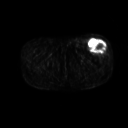
FDG PET of an extremity soft-tissue mass (from a PET/CT study), one axial slice; position 232 of 267 along the scan axis; 3.27 mm slice thickness; 128 × 128 image matrix, field of view 500 × 500 mm. Patient: male, 64 years. Case-level facts recorded for this patient, not image findings: histological type: extraskeletal osteosarcoma; grade: high; site of the primary tumour: thigh.
Annotated regions visible in this slice (expert contour drawn on MRI and transferred to this co-registered scan by the dataset authors):
- gross tumour volume (mass): bounding box (x1, y1, x2, y2) in pixels: (88, 40, 107, 53)